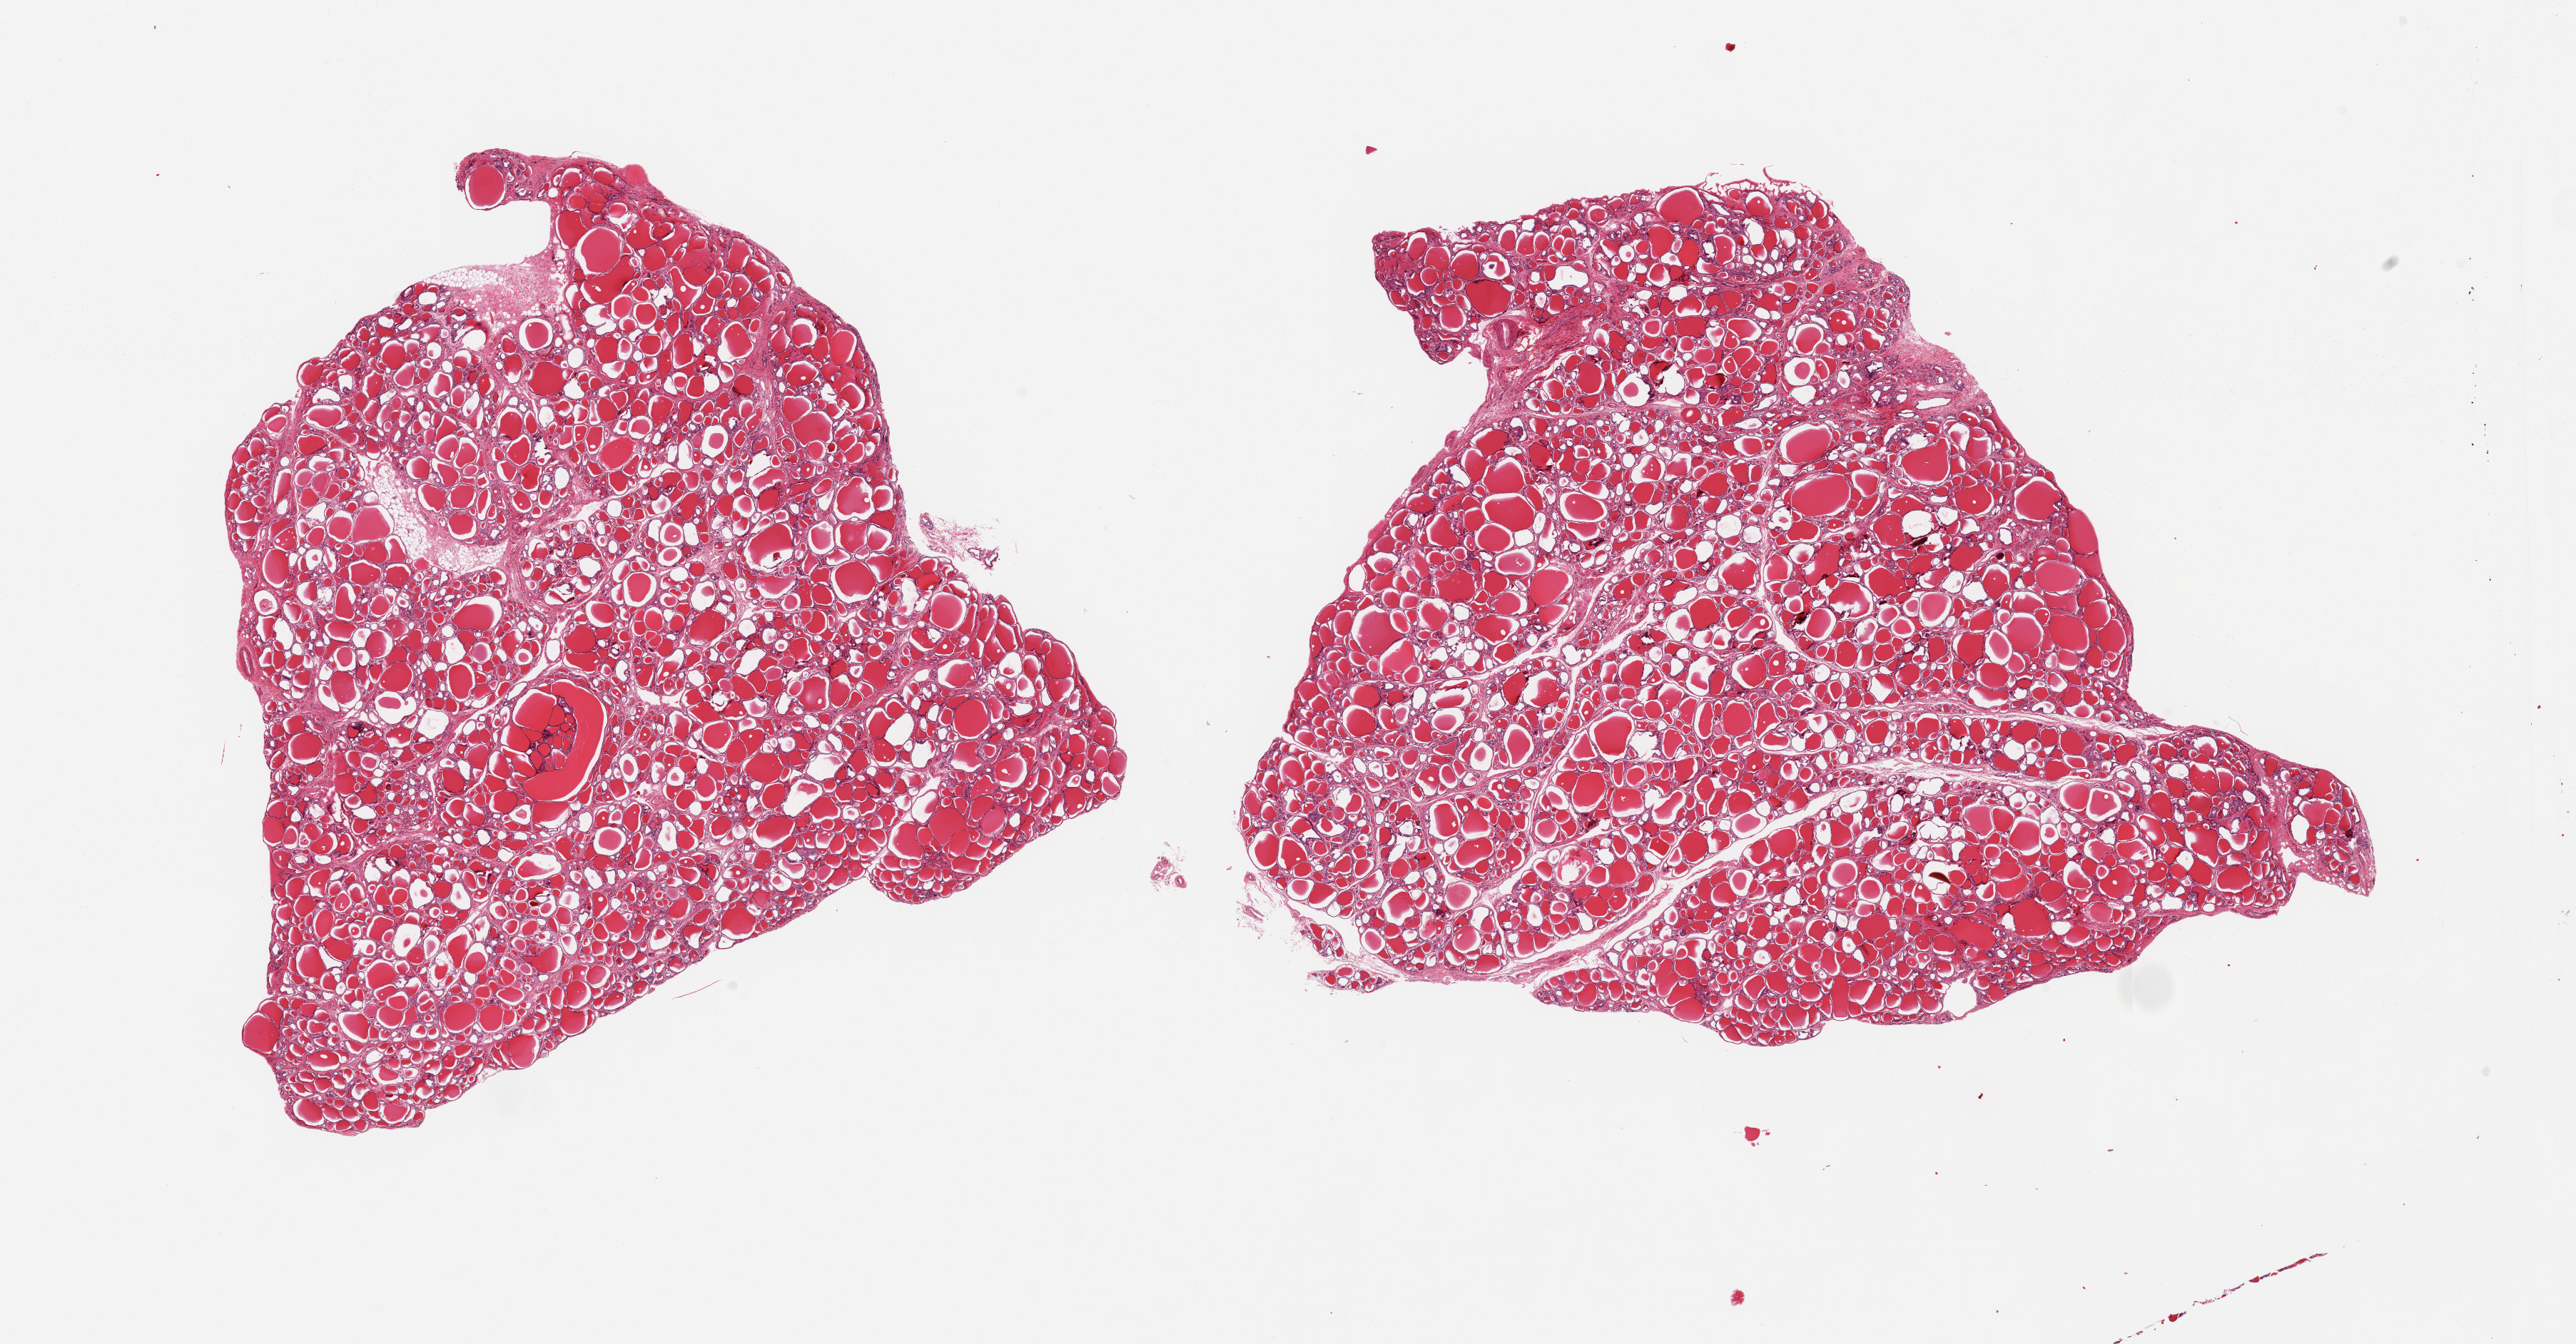
H&E whole-slide image, brightfield — shown as a low-resolution overview of the whole scanned area (about 28.5 x 14.9 mm). PAXgene-fixed paraffin-embedded (PFPE) section. Target tissue: thyroid. Tissue donor sample. Donor: male.
- review note (as recorded): 2 pieces small (~1.5mm) colloid cyst